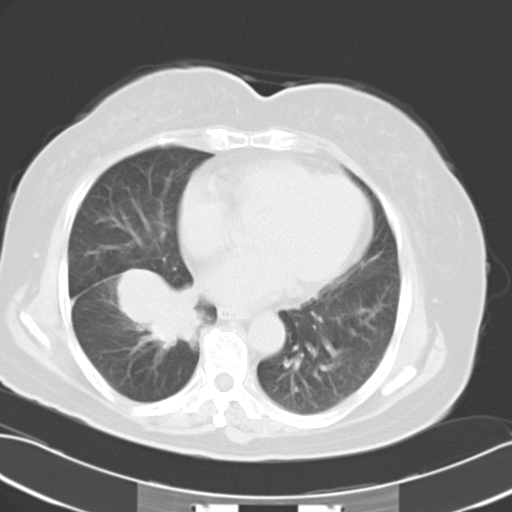
Chest CT, one axial slice; slice 11 of 24 in the series (ordered by position); 120 kVp; lung window (W 1500 / L -600 HU); 10 mm slice thickness; 512 × 512 image matrix. Patient: female, 63 years. Case-level facts recorded for this patient, not image findings: clinical TNM (as recorded): T3 N0 M0.
Structures marked on this image (rectangle marked by the reading radiologist):
- lung tumour (recorded histology: adenocarcinoma): bounding box [x1, y1, x2, y2] px = [107, 250, 207, 351]